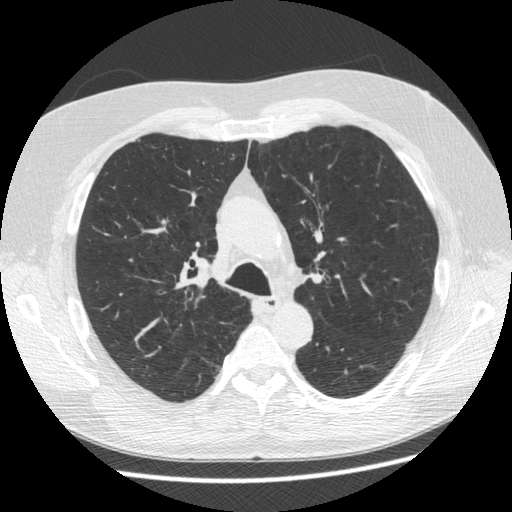
Axial slice from a low-dose chest CT screening exam, third annual screen, lung window (W 1500 / L -600 HU), 1.25 mm slice thickness, standard (soft-tissue) reconstruction kernel (STANDARD), 120 kVp, slice 169 of 545 in the series. Male, age 63 years at enrolment. Former smoker at enrolment.
• Lesion marked by an expert reader, bounding box (x1, y1, x2, y2) in pixels: (150, 209, 182, 239).
• The screening reader recorded 2 non-calcified nodules or masses ≥4 mm on this exam; which of them this box marks is not recorded.
• Later outcome: lung cancer diagnosed 342 days after this screen — adenocarcinoma, NOS, right upper lobe, stage IIA (AJCC 6th edition), 8 mm at pathology.